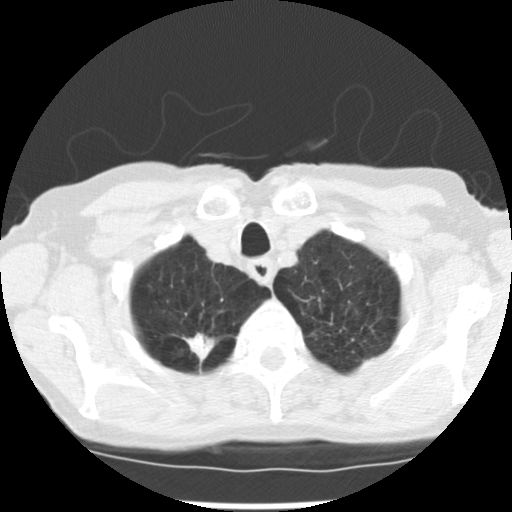
Axial slice from a low-dose chest CT screening exam, first (baseline) screen, lung window (W 1500 / L -600 HU), 2.5 mm slice thickness, standard (soft-tissue) reconstruction kernel (STANDARD). Female participant, aged 72 years at enrolment.
Lesion marked by an expert reader, bounding box (x1, y1, x2, y2) in pixels: (171, 315, 231, 360). The screening reader recorded 3 non-calcified nodules or masses ≥4 mm on this exam (right upper lobe, left upper lobe, left lower lobe); which of them this box marks is not recorded. Participant outcome: lung cancer diagnosed 50 days after this screen — adenocarcinoma, NOS, right upper lobe, moderately differentiated (G2), stage IB (AJCC 6th edition), 22 mm at pathology.